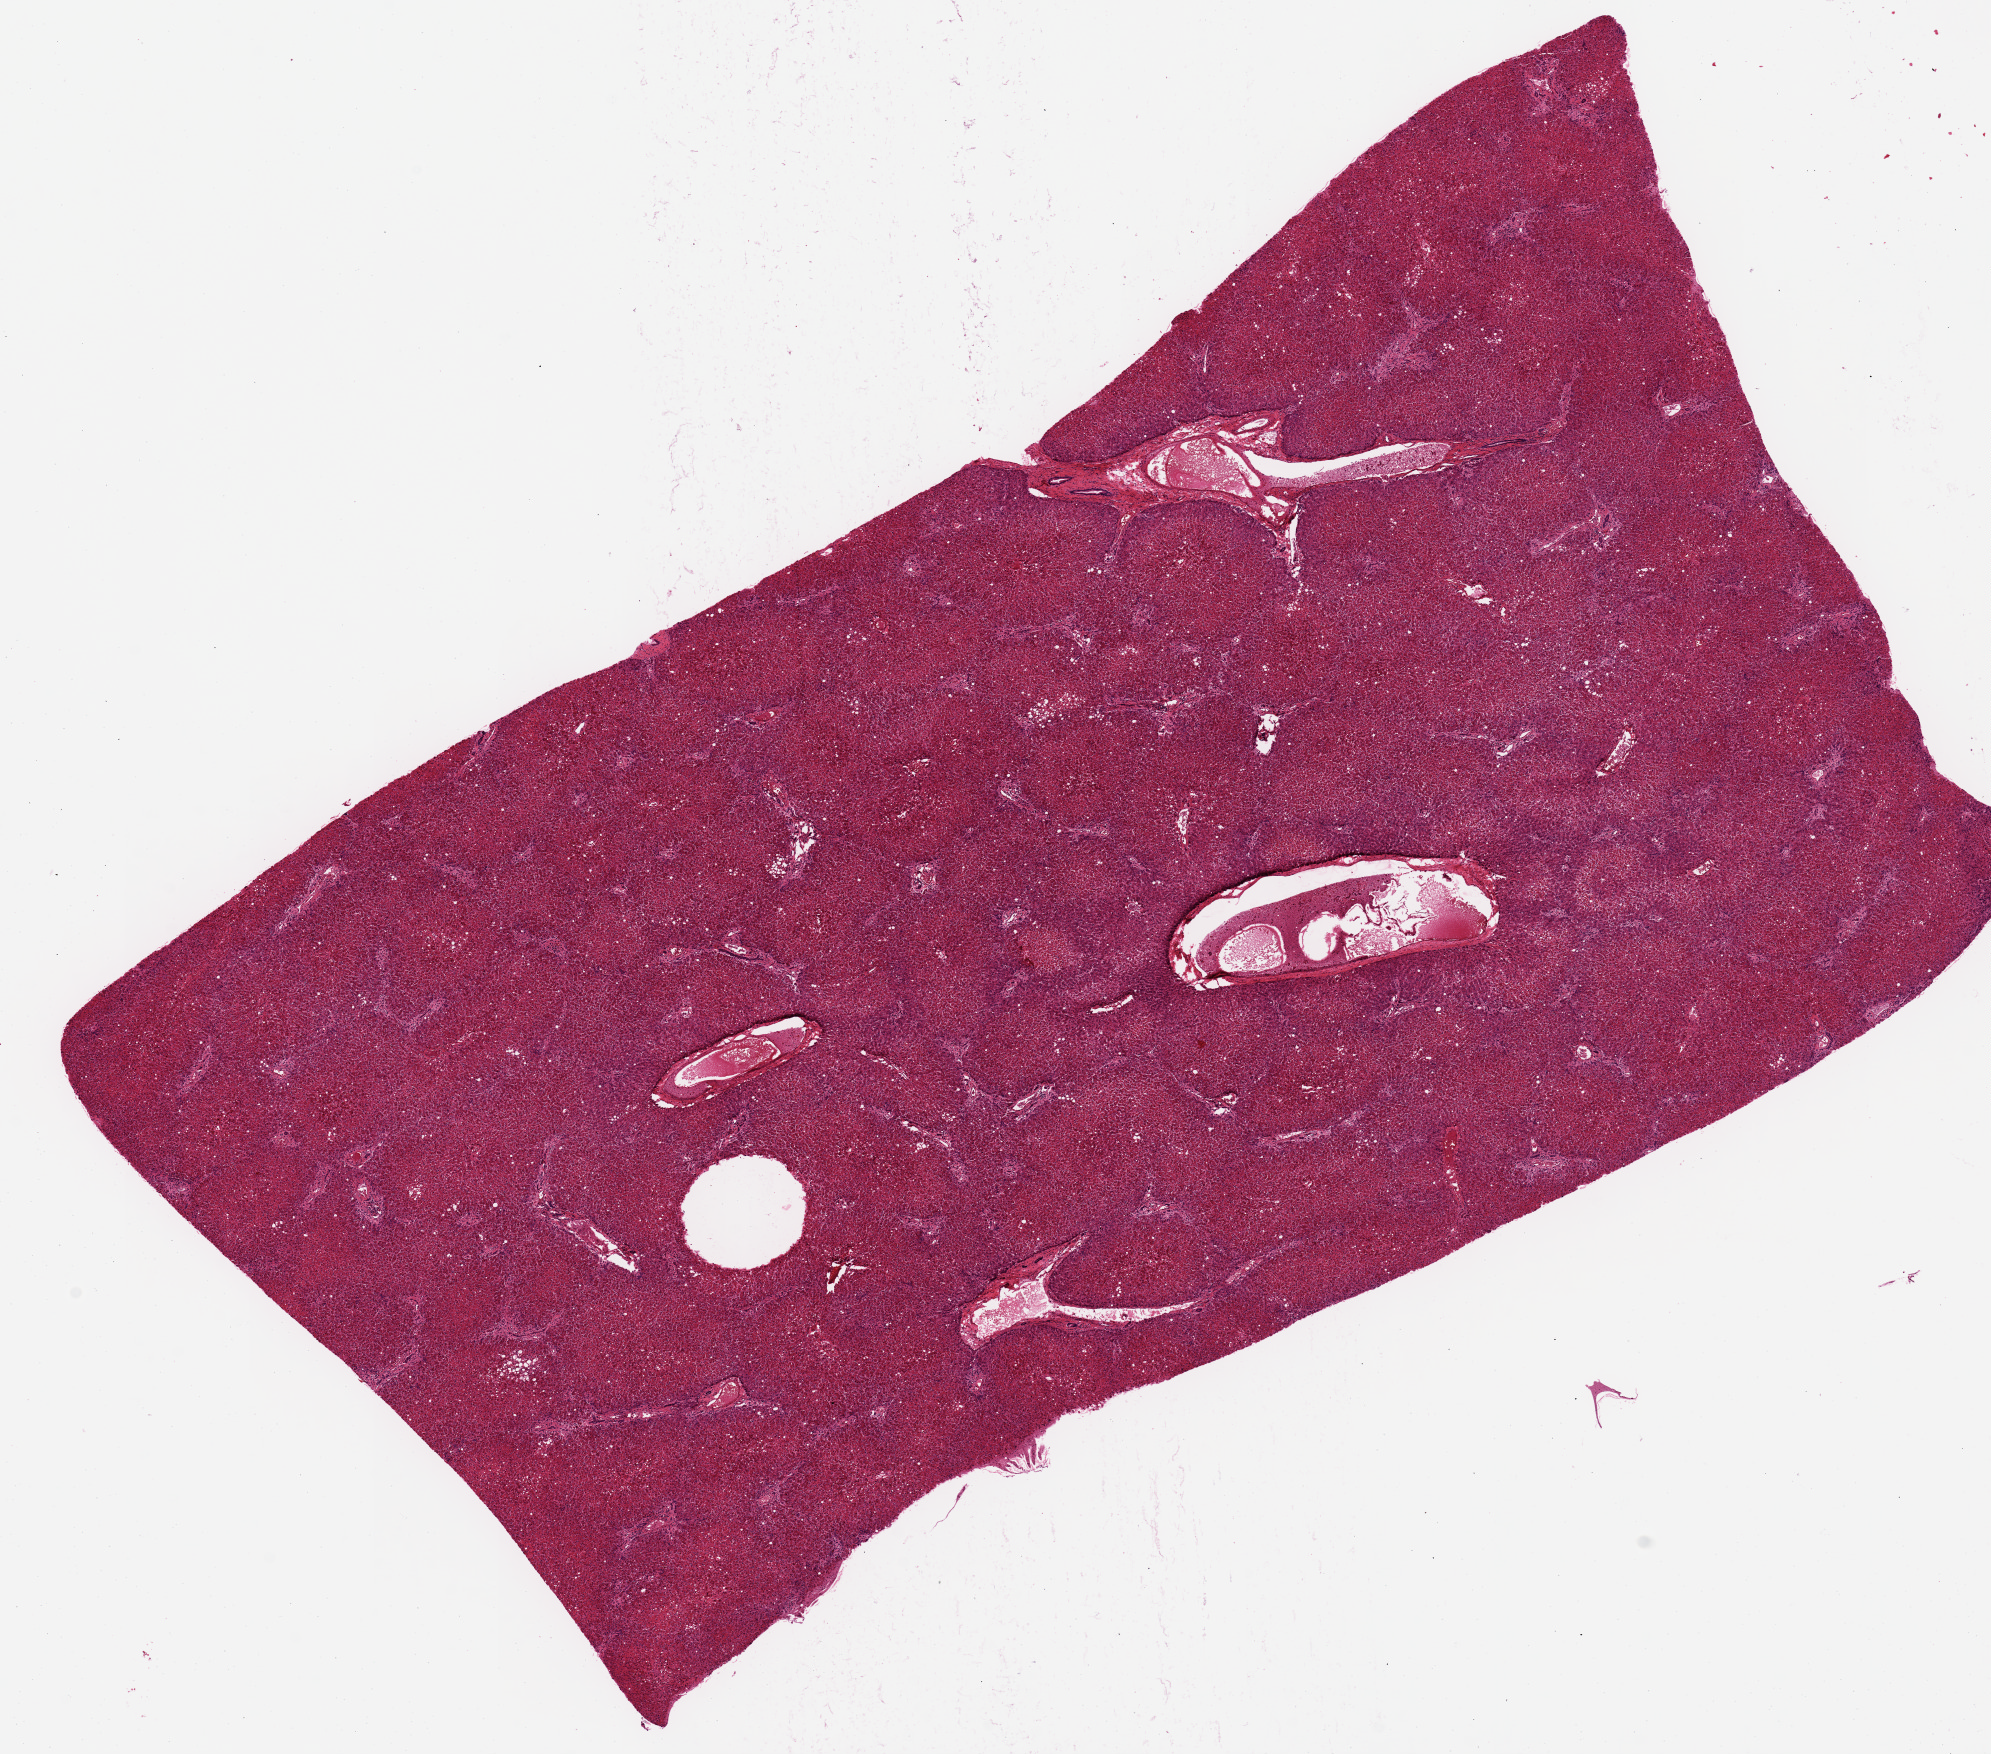
Digitized H&E-stained section, brightfield — whole scanned area (about 15.8 x 13.9 mm, from a 20x scan) shown as a low-resolution overview, PAXgene-fixed paraffin-embedded (PFPE) section, section of liver (target tissue), tissue donor sample. Donor sex: male.
Reviewer comment on this tissue sample: Mild central hypoxia.